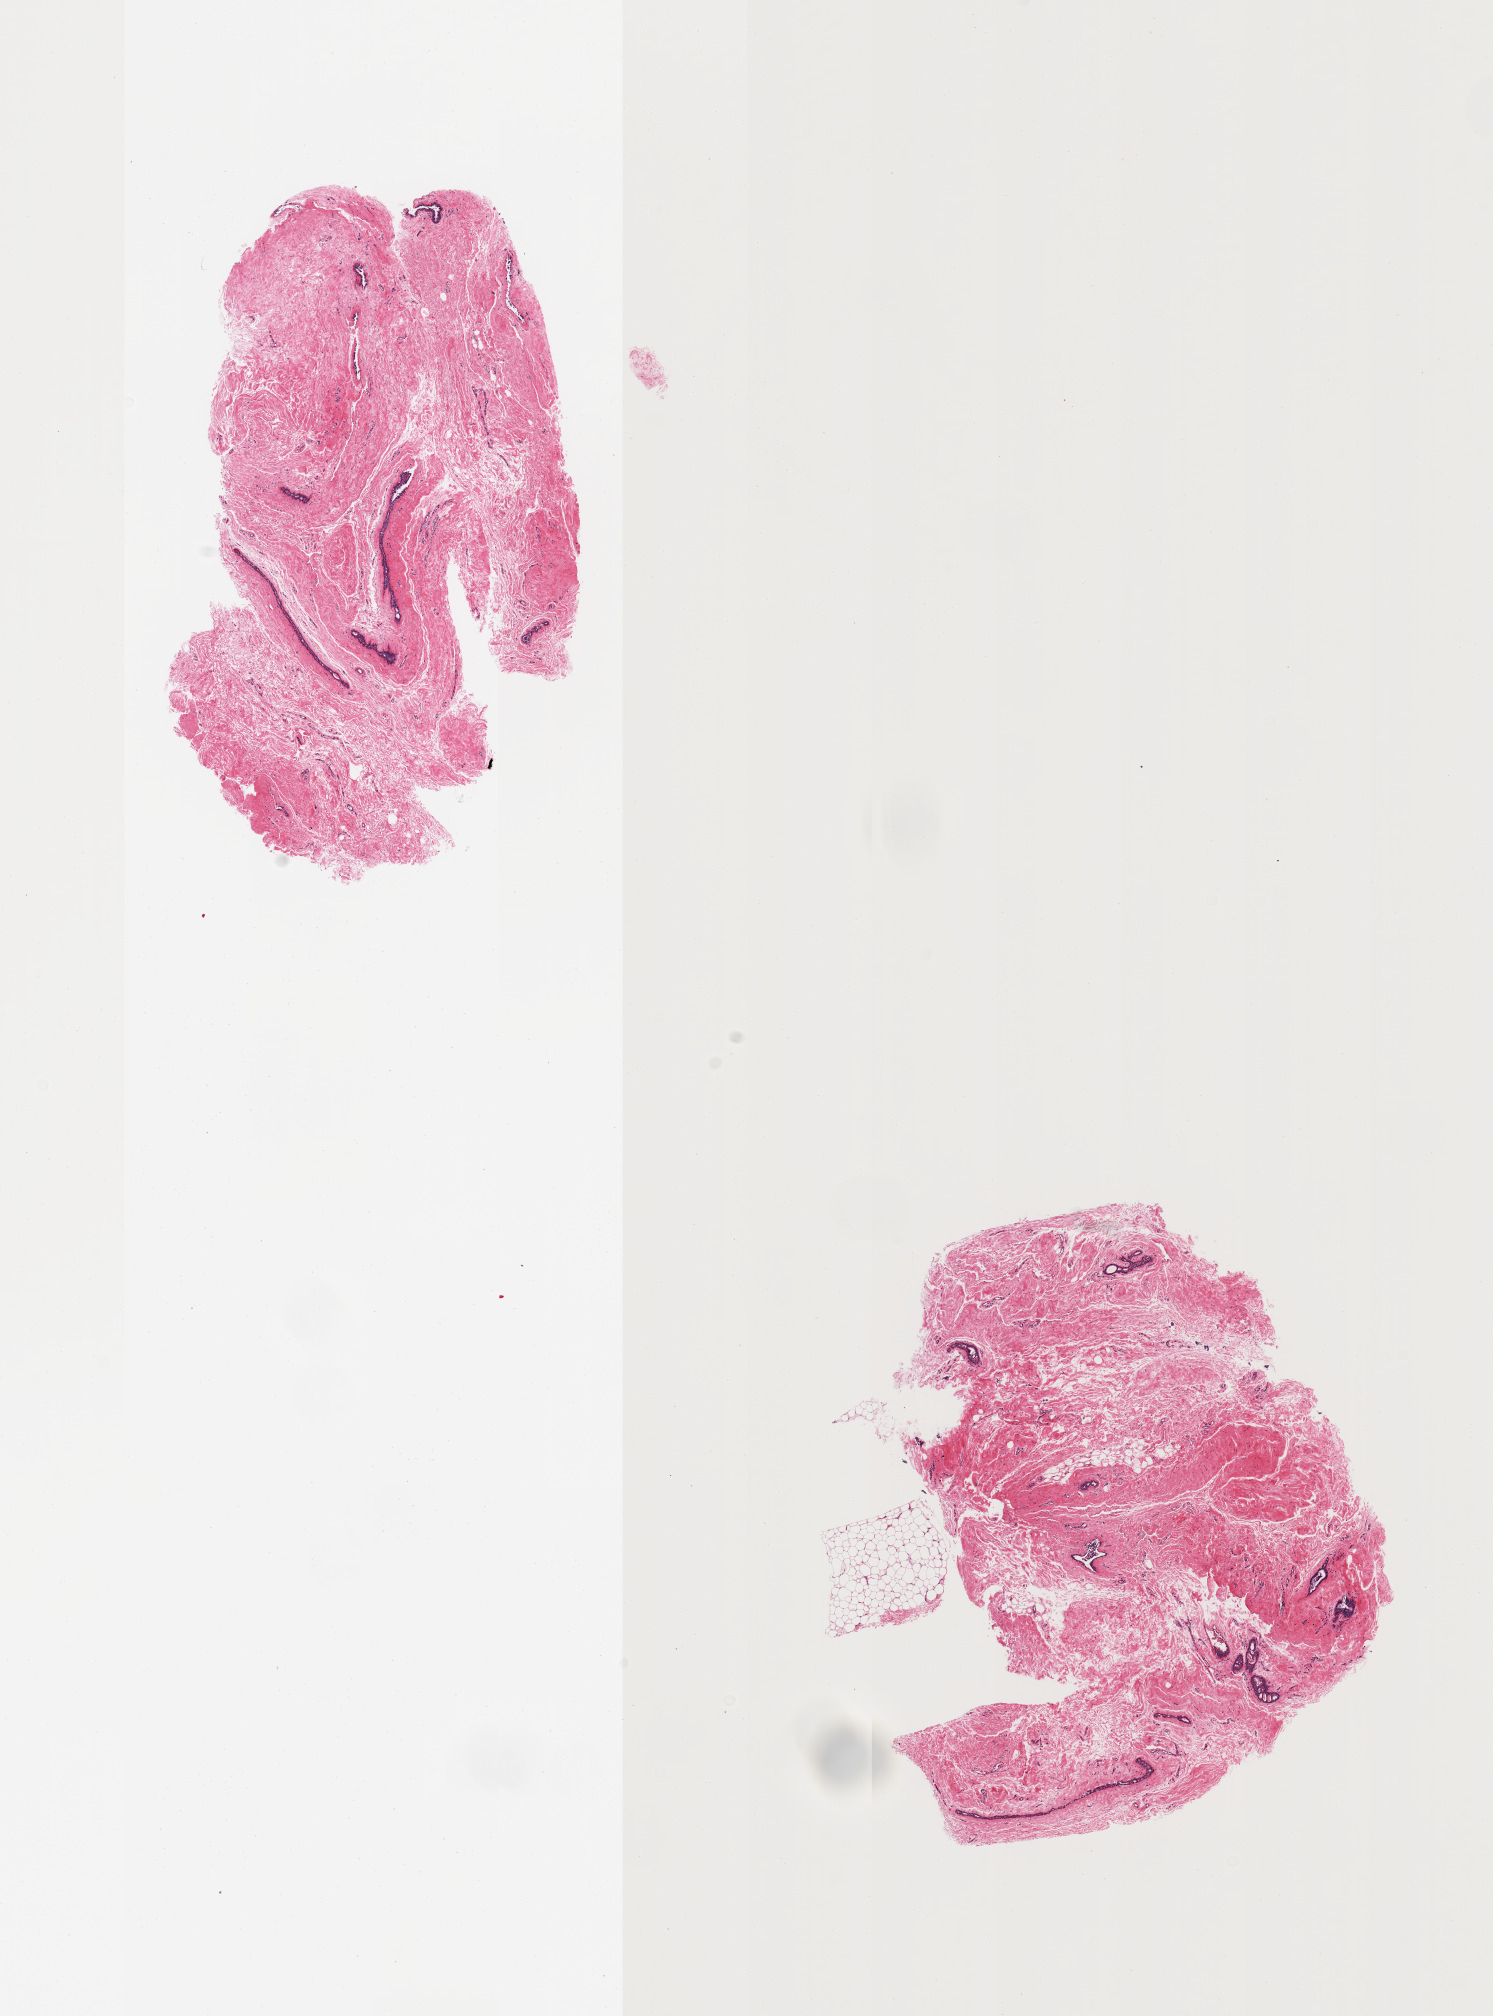
Digitized haematoxylin and eosin-stained section, brightfield, shown as a low-resolution overview of the whole scanned area (about 11.8 x 16.0 mm, slide scanned at 20x). PAXgene-fixed paraffin-embedded (PFPE) section. Target tissue: breast. Tissue donor sample. Donor sex: male.
• review note (as recorded): 2 pieces, gynecomastoid stromal/ductal hyperplasia